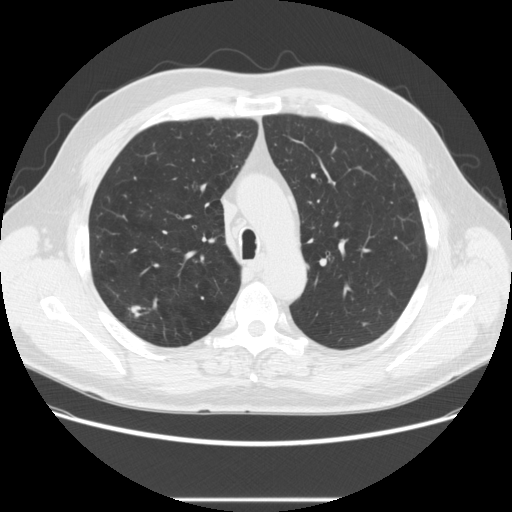
Low-dose screening chest CT, axial slice; baseline screening round; lung window (W 1500 / L -600 HU); standard (soft-tissue) reconstruction kernel (STANDARD); slice 77 of 270 in the series; 512 × 512 image matrix. Male participant, aged 64 years at enrolment. Former smoker at enrolment.
Lesion marked by an expert reader, bounding box [x1, y1, x2, y2] px = [117, 298, 152, 326]. The screening reader recorded 2 non-calcified nodules or masses ≥4 mm on this exam; which of them this box marks is not recorded. Participant outcome: lung cancer diagnosed 753 days after this screen — adenocarcinoma, NOS, right upper lobe, moderately differentiated (G2), stage IA (AJCC 6th edition), 14 mm at pathology.